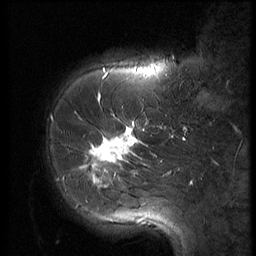
Breast MRI (dynamic contrast-enhanced), one sagittal slice; slice 18 of 56 in the series (ordered by position); 3 images stored at this slice position (order not interpretable as contrast timing); 1.5 T; TE 4.2 ms, TR 9 ms; 2.5 mm slice thickness; 256 × 256 image matrix. Female patient, age 61 years. Case-level facts recorded for this patient, not image findings: setting: breast cancer imaged before/during neoadjuvant chemotherapy; receptor status: HR-positive, HER2-negative.
Structures marked on this image (semi-automatic segmentation, software-assisted and operator-edited):
- analysis volume of interest (the breast-tissue region the enhancement analysis was run in; not a lesion): box from (x=47, y=89) to (x=153, y=191) px
- tumour enhancement mask (voxels above the 140 % enhancement threshold inside the analysis volume of interest): (x=81, y=98)–(x=144, y=188)